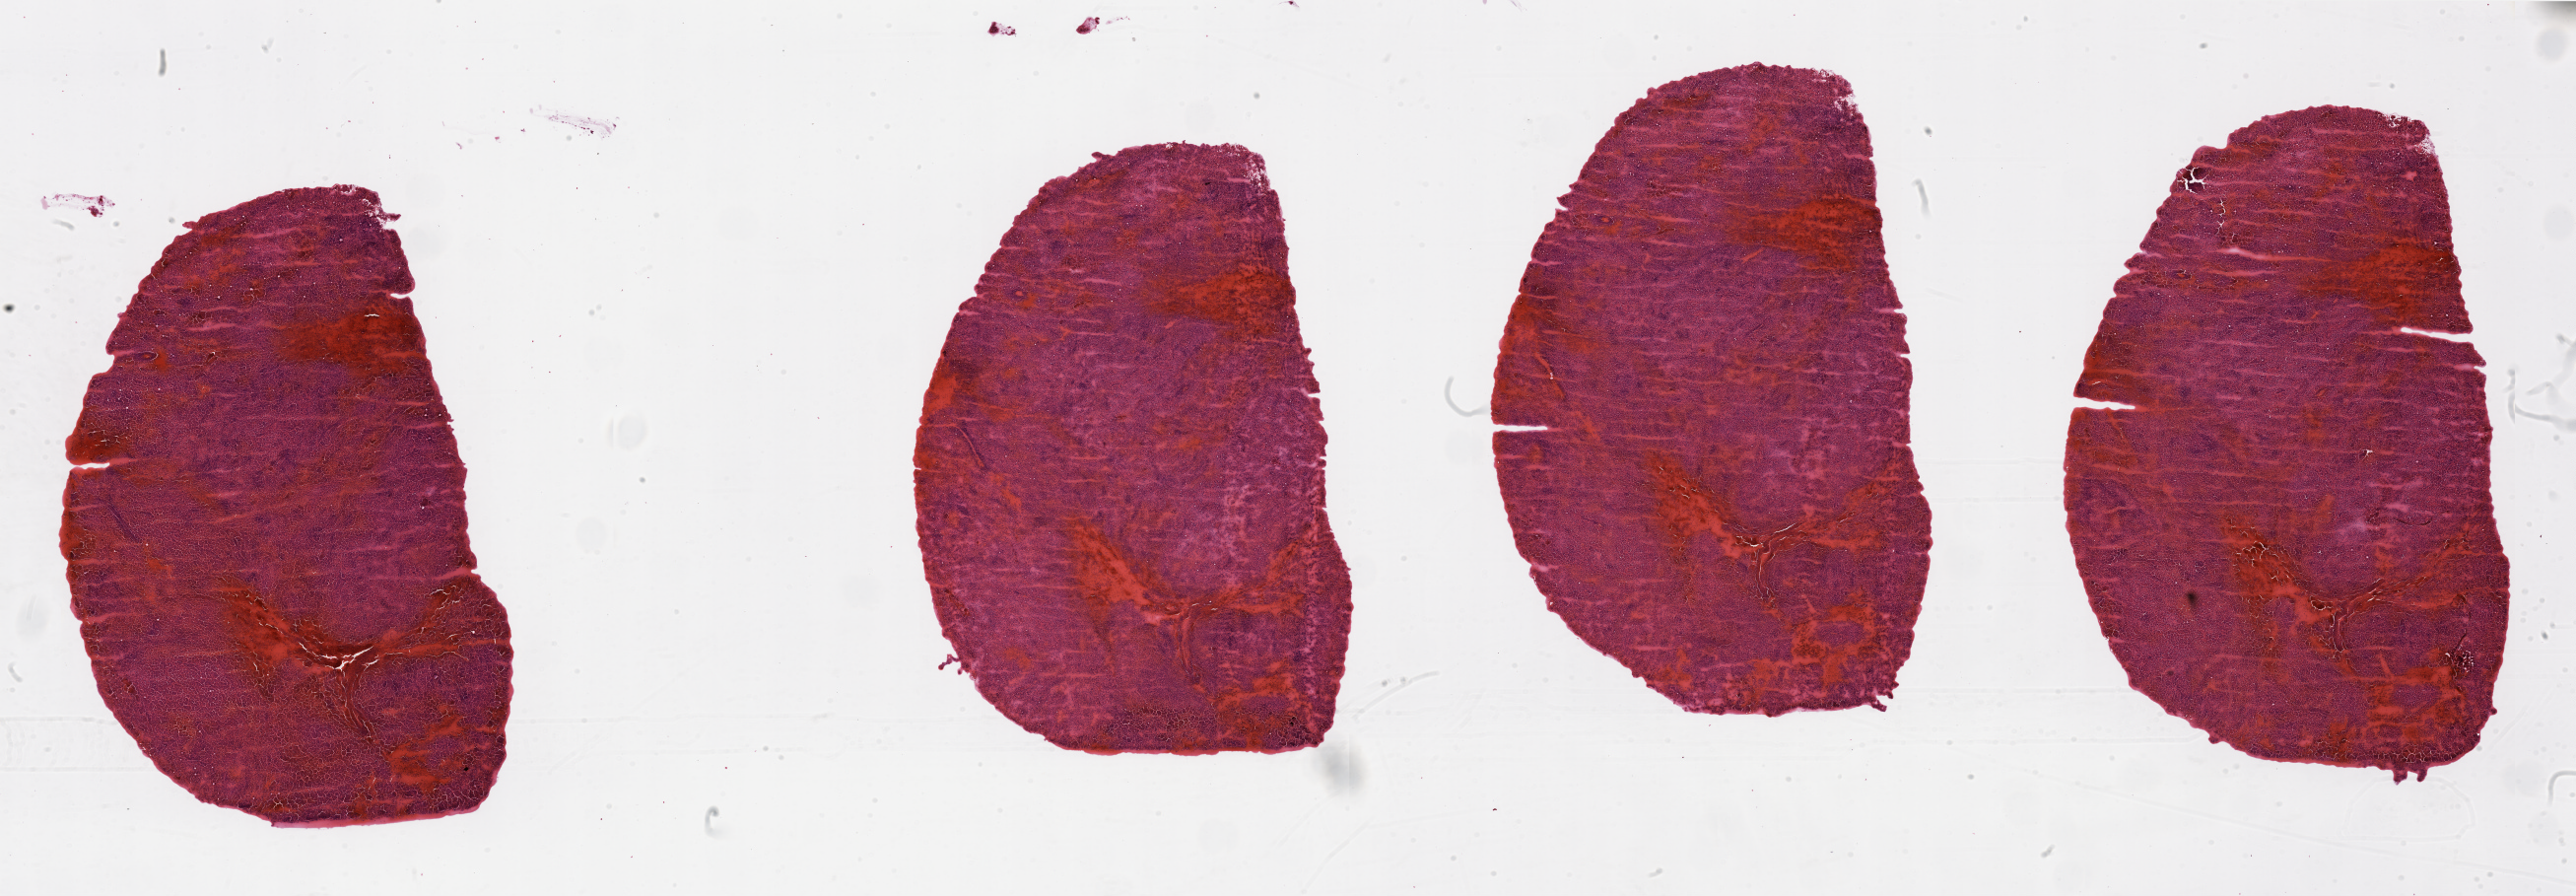
Digitized H&E-stained tissue section (whole slide), whole scanned area (about 41.3 x 14.4 mm, slide scanned at 20x) shown as a low-resolution overview, tumour tissue sample, kidney. 68-year-old male patient. Histologic grade: G3 (poorly differentiated).
* diagnosis: Renal cell carcinoma, NOS
* AJCC pathologic stage: I
* primary tumour site (as recorded): lower pole